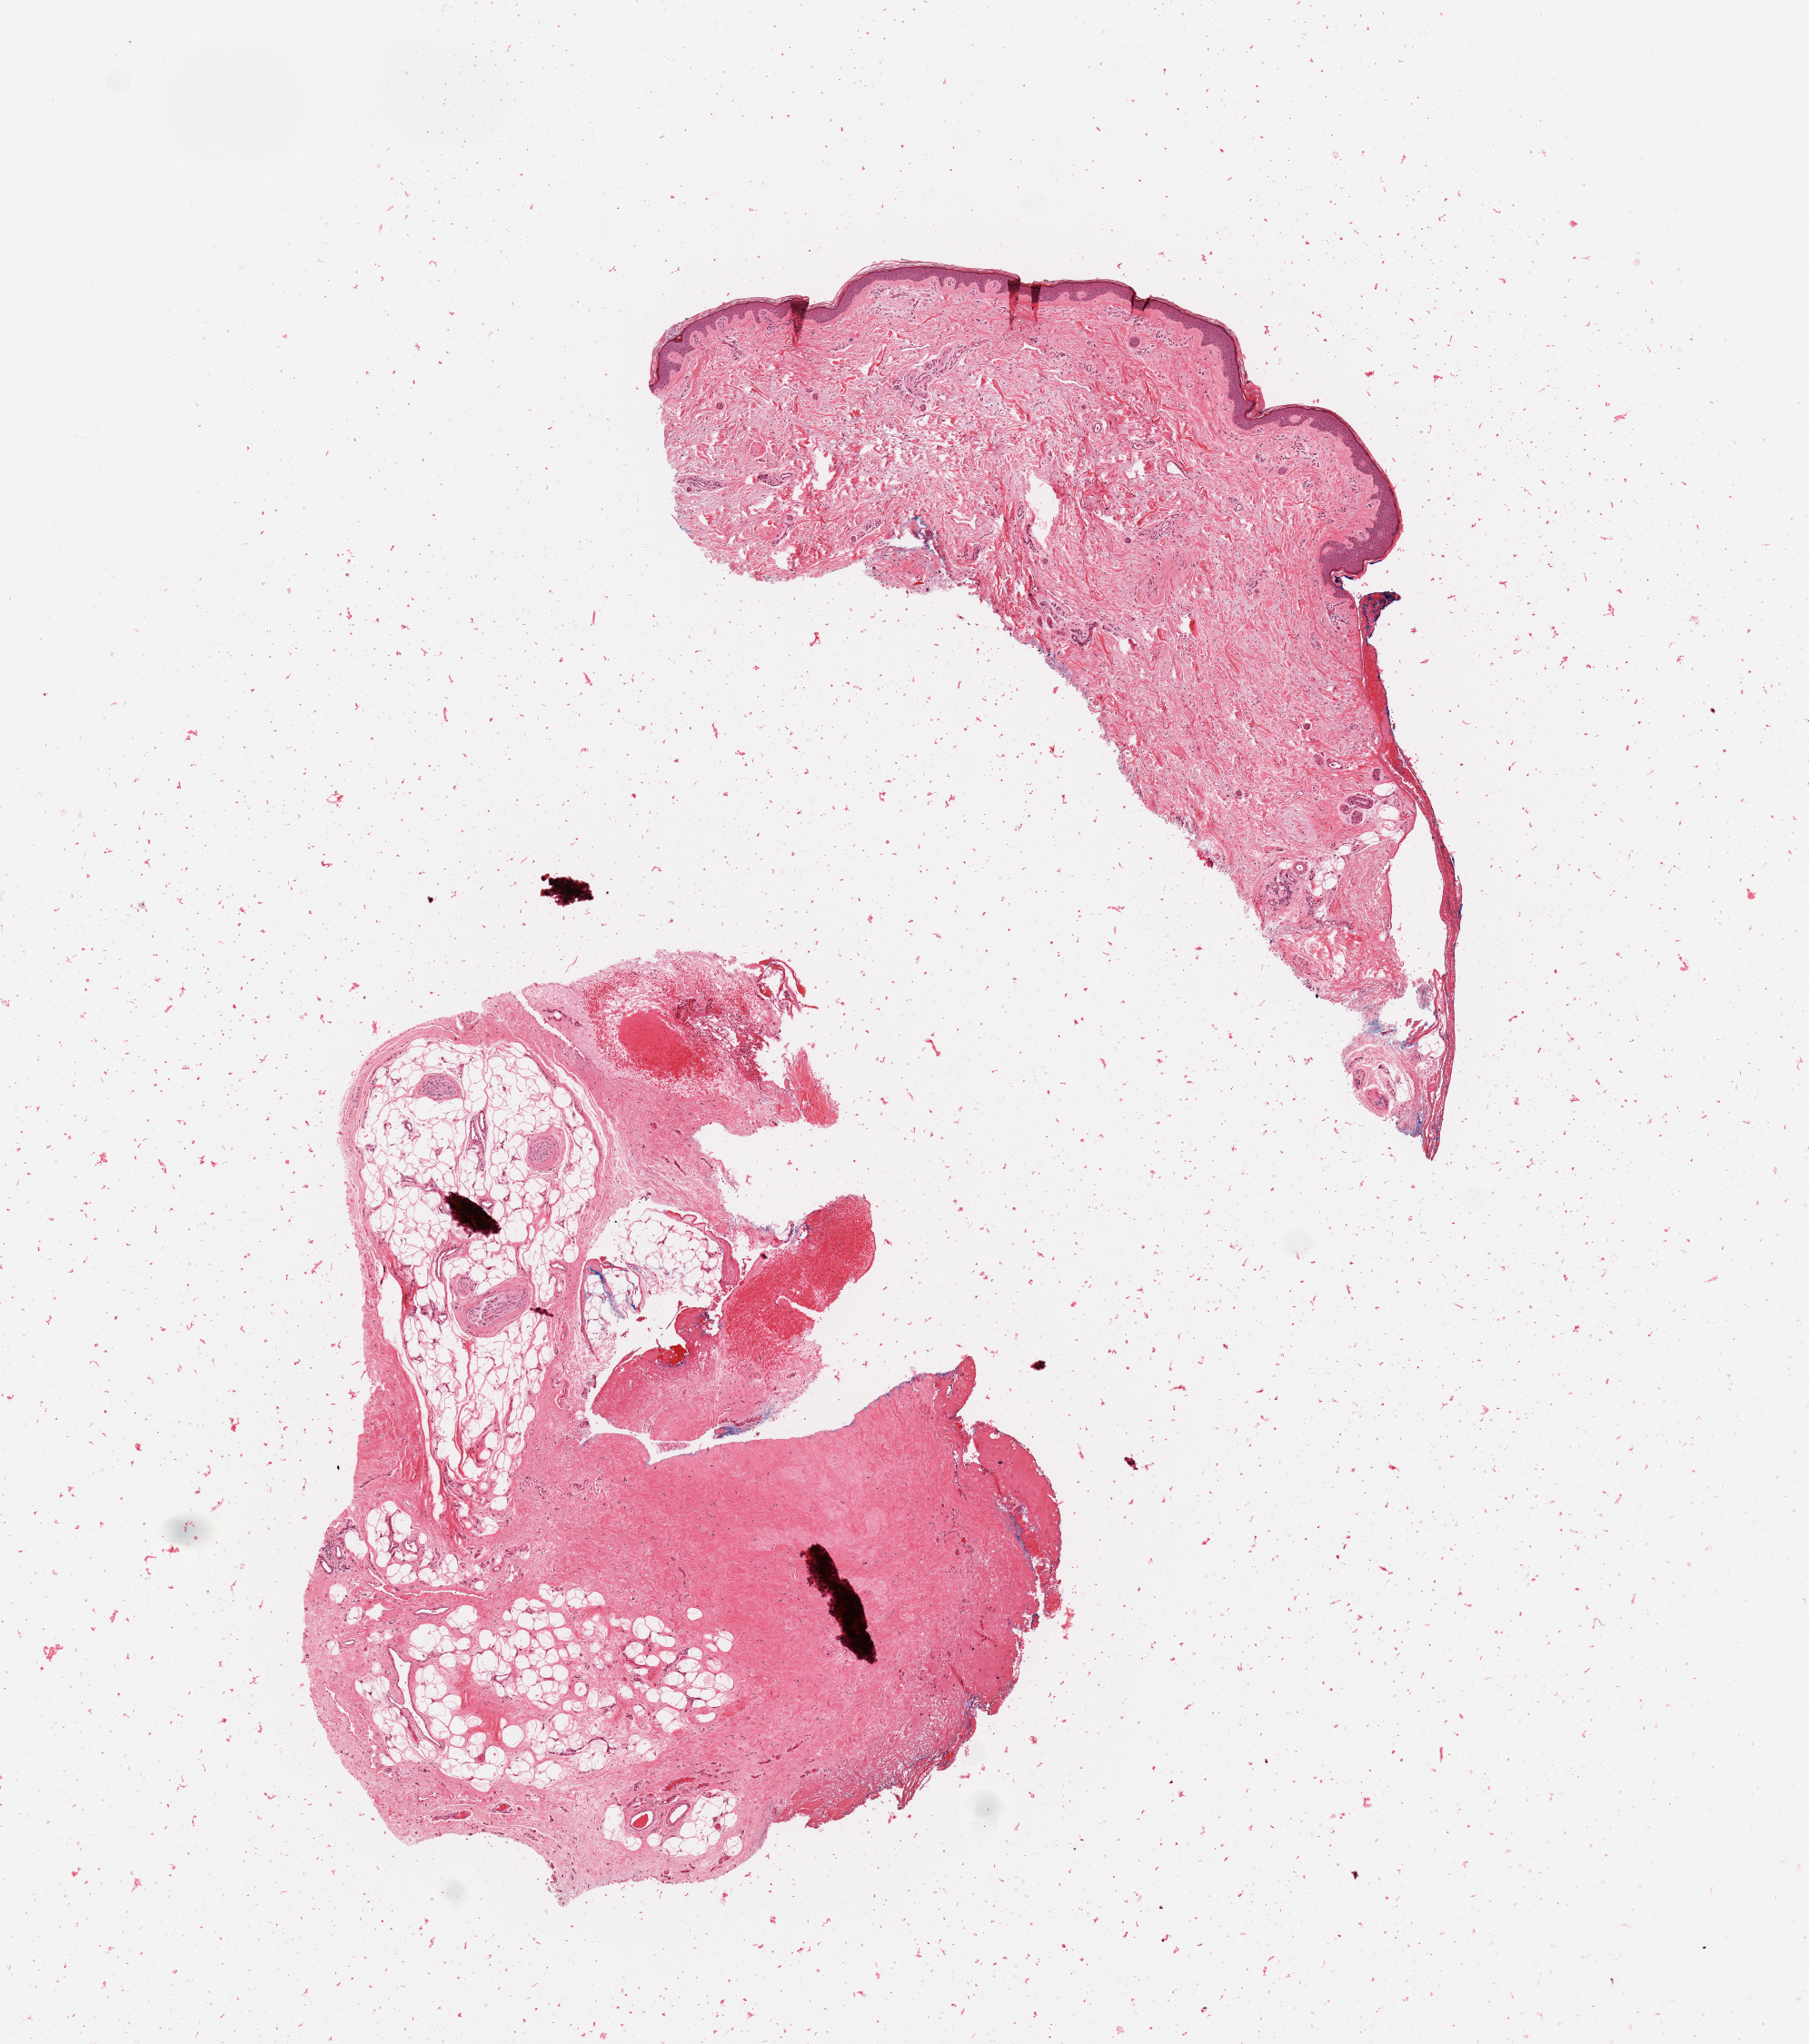
Whole-slide histology image, Hematoxylin and eosin (H&E) stained, whole scanned area (about 7.9 x 8.9 mm) shown as a low-resolution overview; normal (non-tumour) tissue sample. Patient sex: female.
This section: normal (non-tumour) tissue from the same patient. Patient diagnosis (cohort enrolment): sarcoma (site not recorded at cohort level).